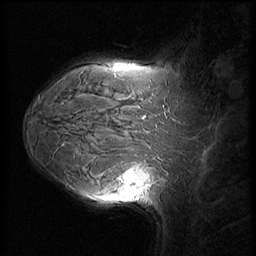
Breast MRI (dynamic contrast-enhanced), one sagittal slice; position 44 of 60 along the scan axis; dynamic contrast-enhanced series, image 2 of 3 at this slice position (ordered by acquisition); 1.5 T; TE 4.2 ms, TR 8.9 ms; 2.5 mm slice thickness; 256 × 256 image matrix, field of view 220 × 220 mm. Patient: female, 37 years. Case-level facts recorded for this patient, not image findings: setting: breast cancer imaged before/during neoadjuvant chemotherapy; receptor status: triple-negative.
Outlined on this slice (semi-automatically segmented with operator editing):
- analysis volume of interest (the breast-tissue region the enhancement analysis was run in; not a lesion): bounding box <114,153,159,206> (left, top, right, bottom; pixels)
- tumour enhancement mask (voxels above the 140 % enhancement threshold inside the analysis volume of interest): <122,169,151,189>